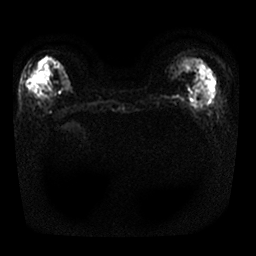
Breast MRI, one axial slice. Position 9 of 25 along the scan axis. Diffusion-weighted series; image 2 of 4 stored at this slice position (different b-values; order by instance number). 1.5 T. 4 mm slice thickness. 256 × 256 image matrix, field of view 340 × 340 mm. Female patient.
Structures marked on this image (manually delineated by an expert):
- tumour on diffusion-weighted imaging: box from (x=36, y=65) to (x=44, y=79) px